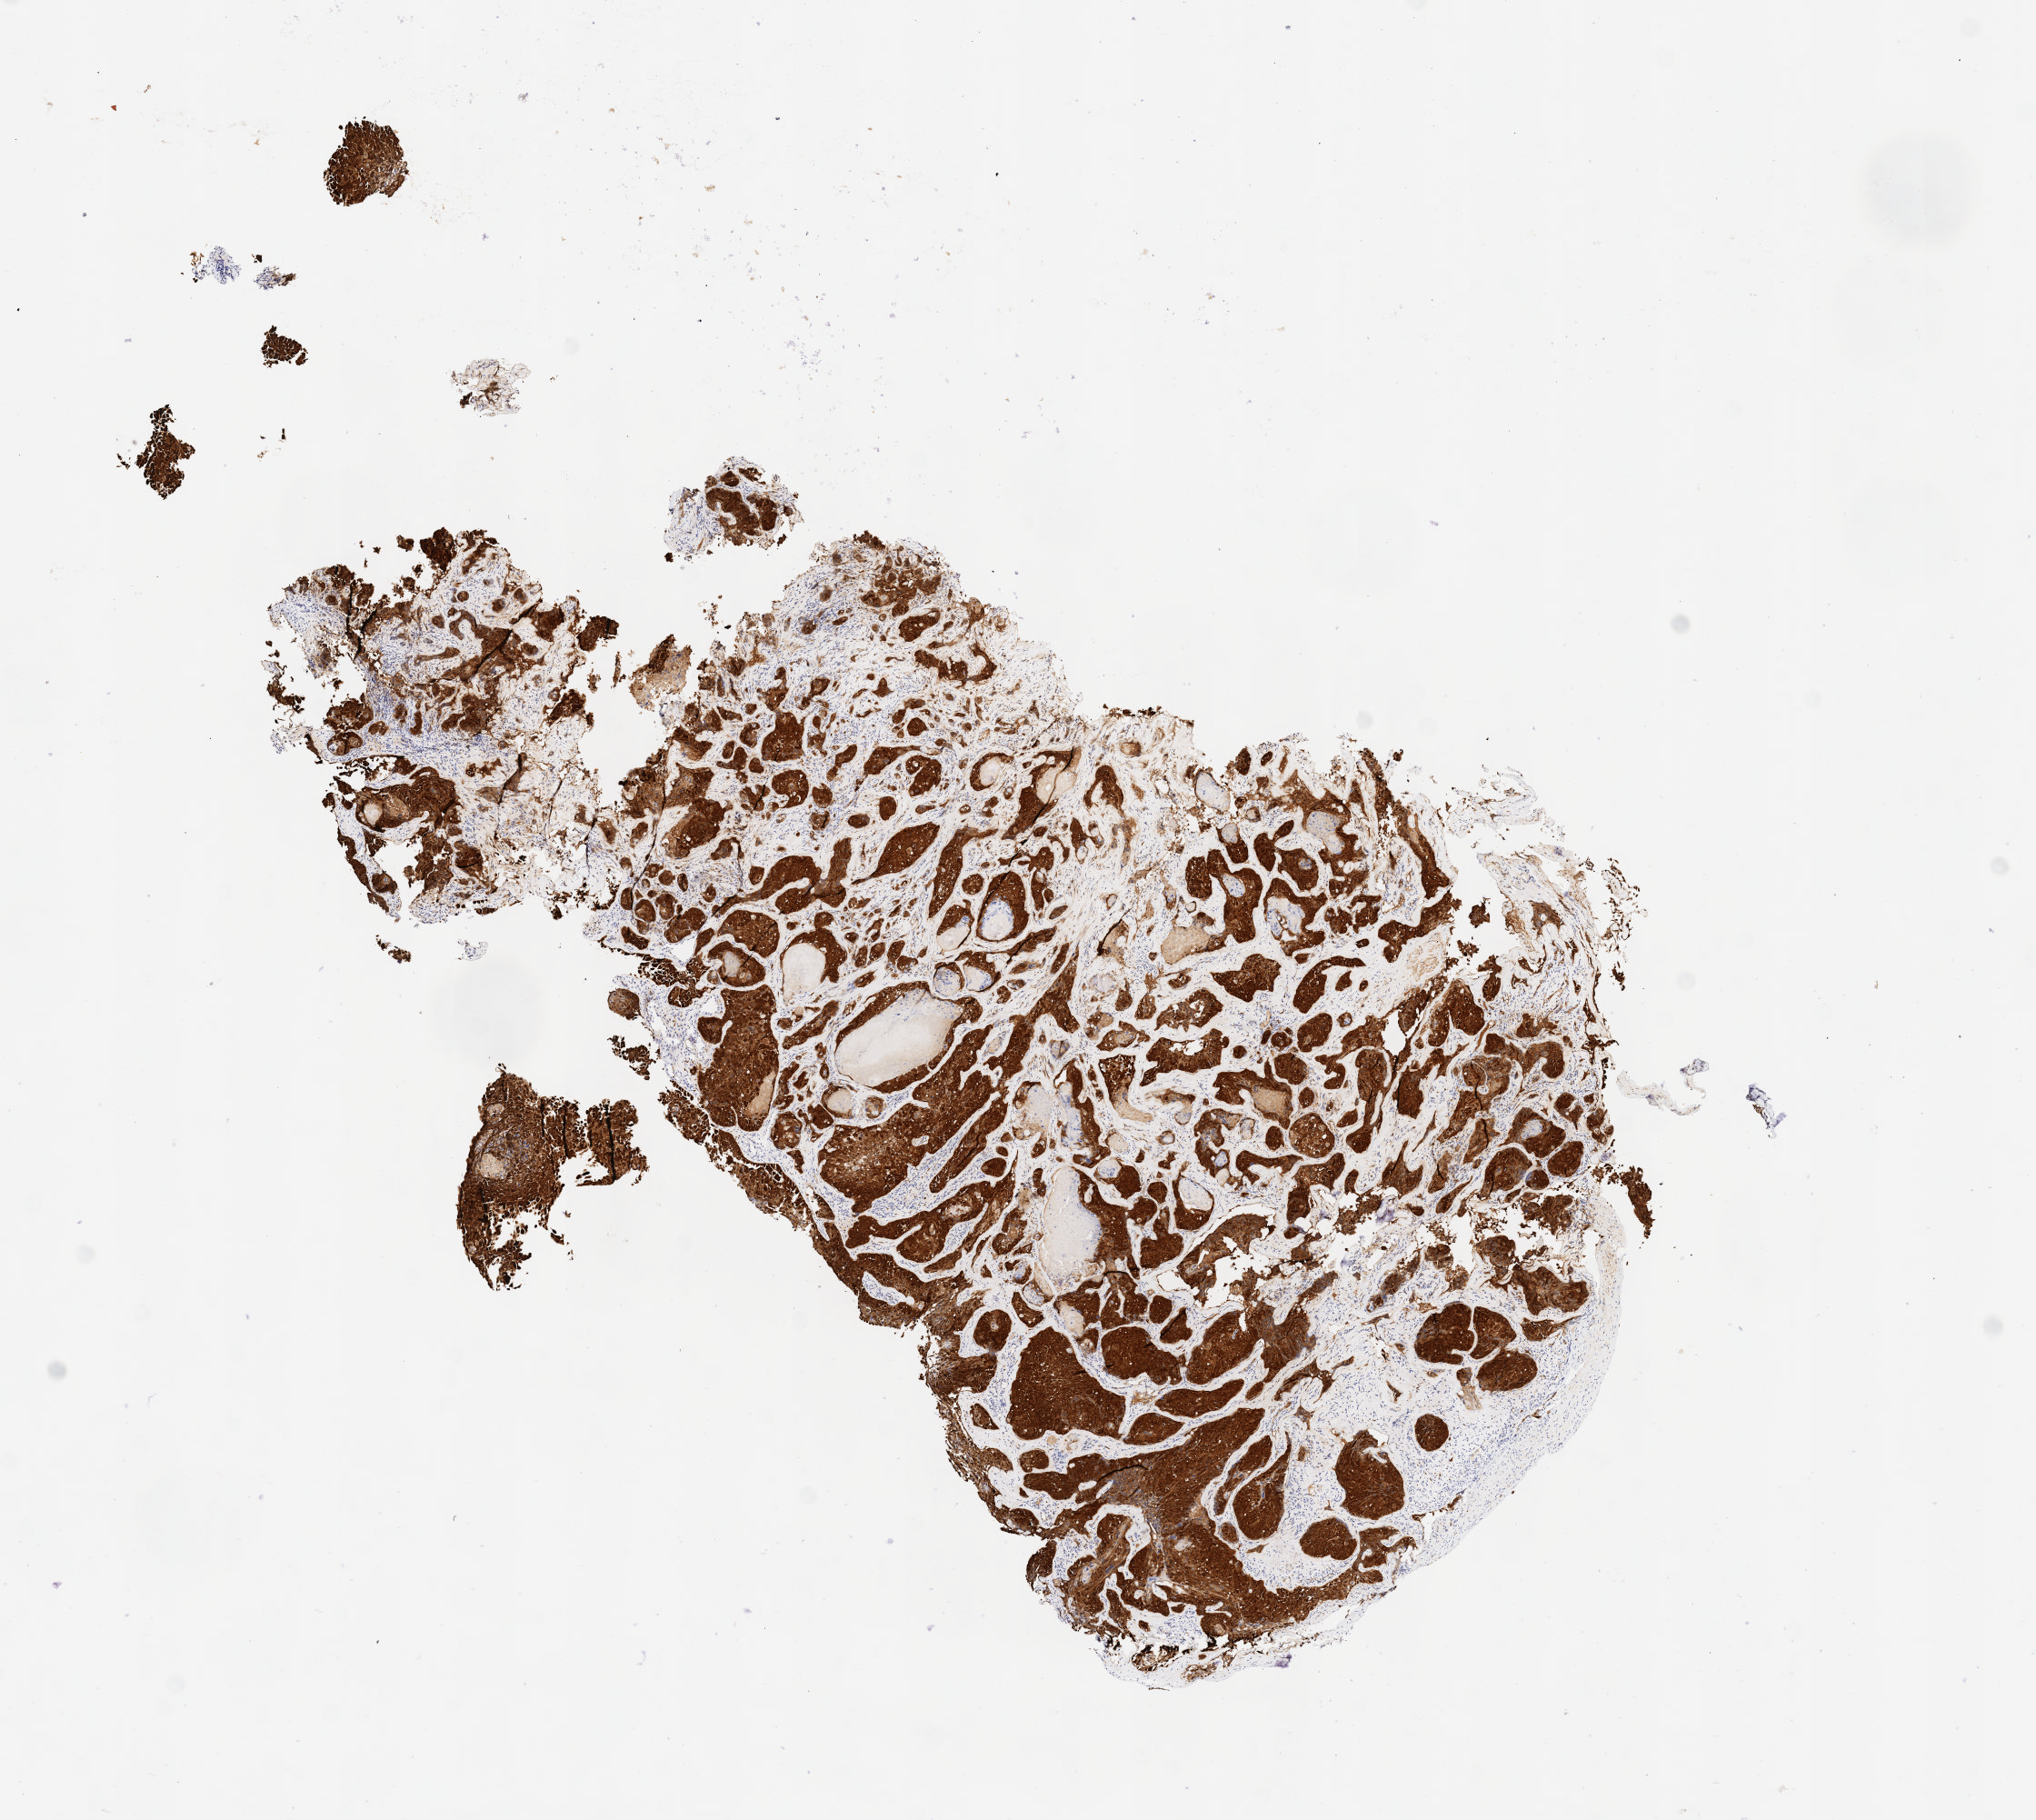
Whole-slide image, immunohistochemical stain for p16 (p16INK4a) — shown as a low-resolution overview of the whole scanned area (about 9.1 x 8.1 mm). Tumor tissue. Site: cervix. Patient female; 67 years old.
Diagnosis: Squamous cell carcinoma, keratinizing, NOS.